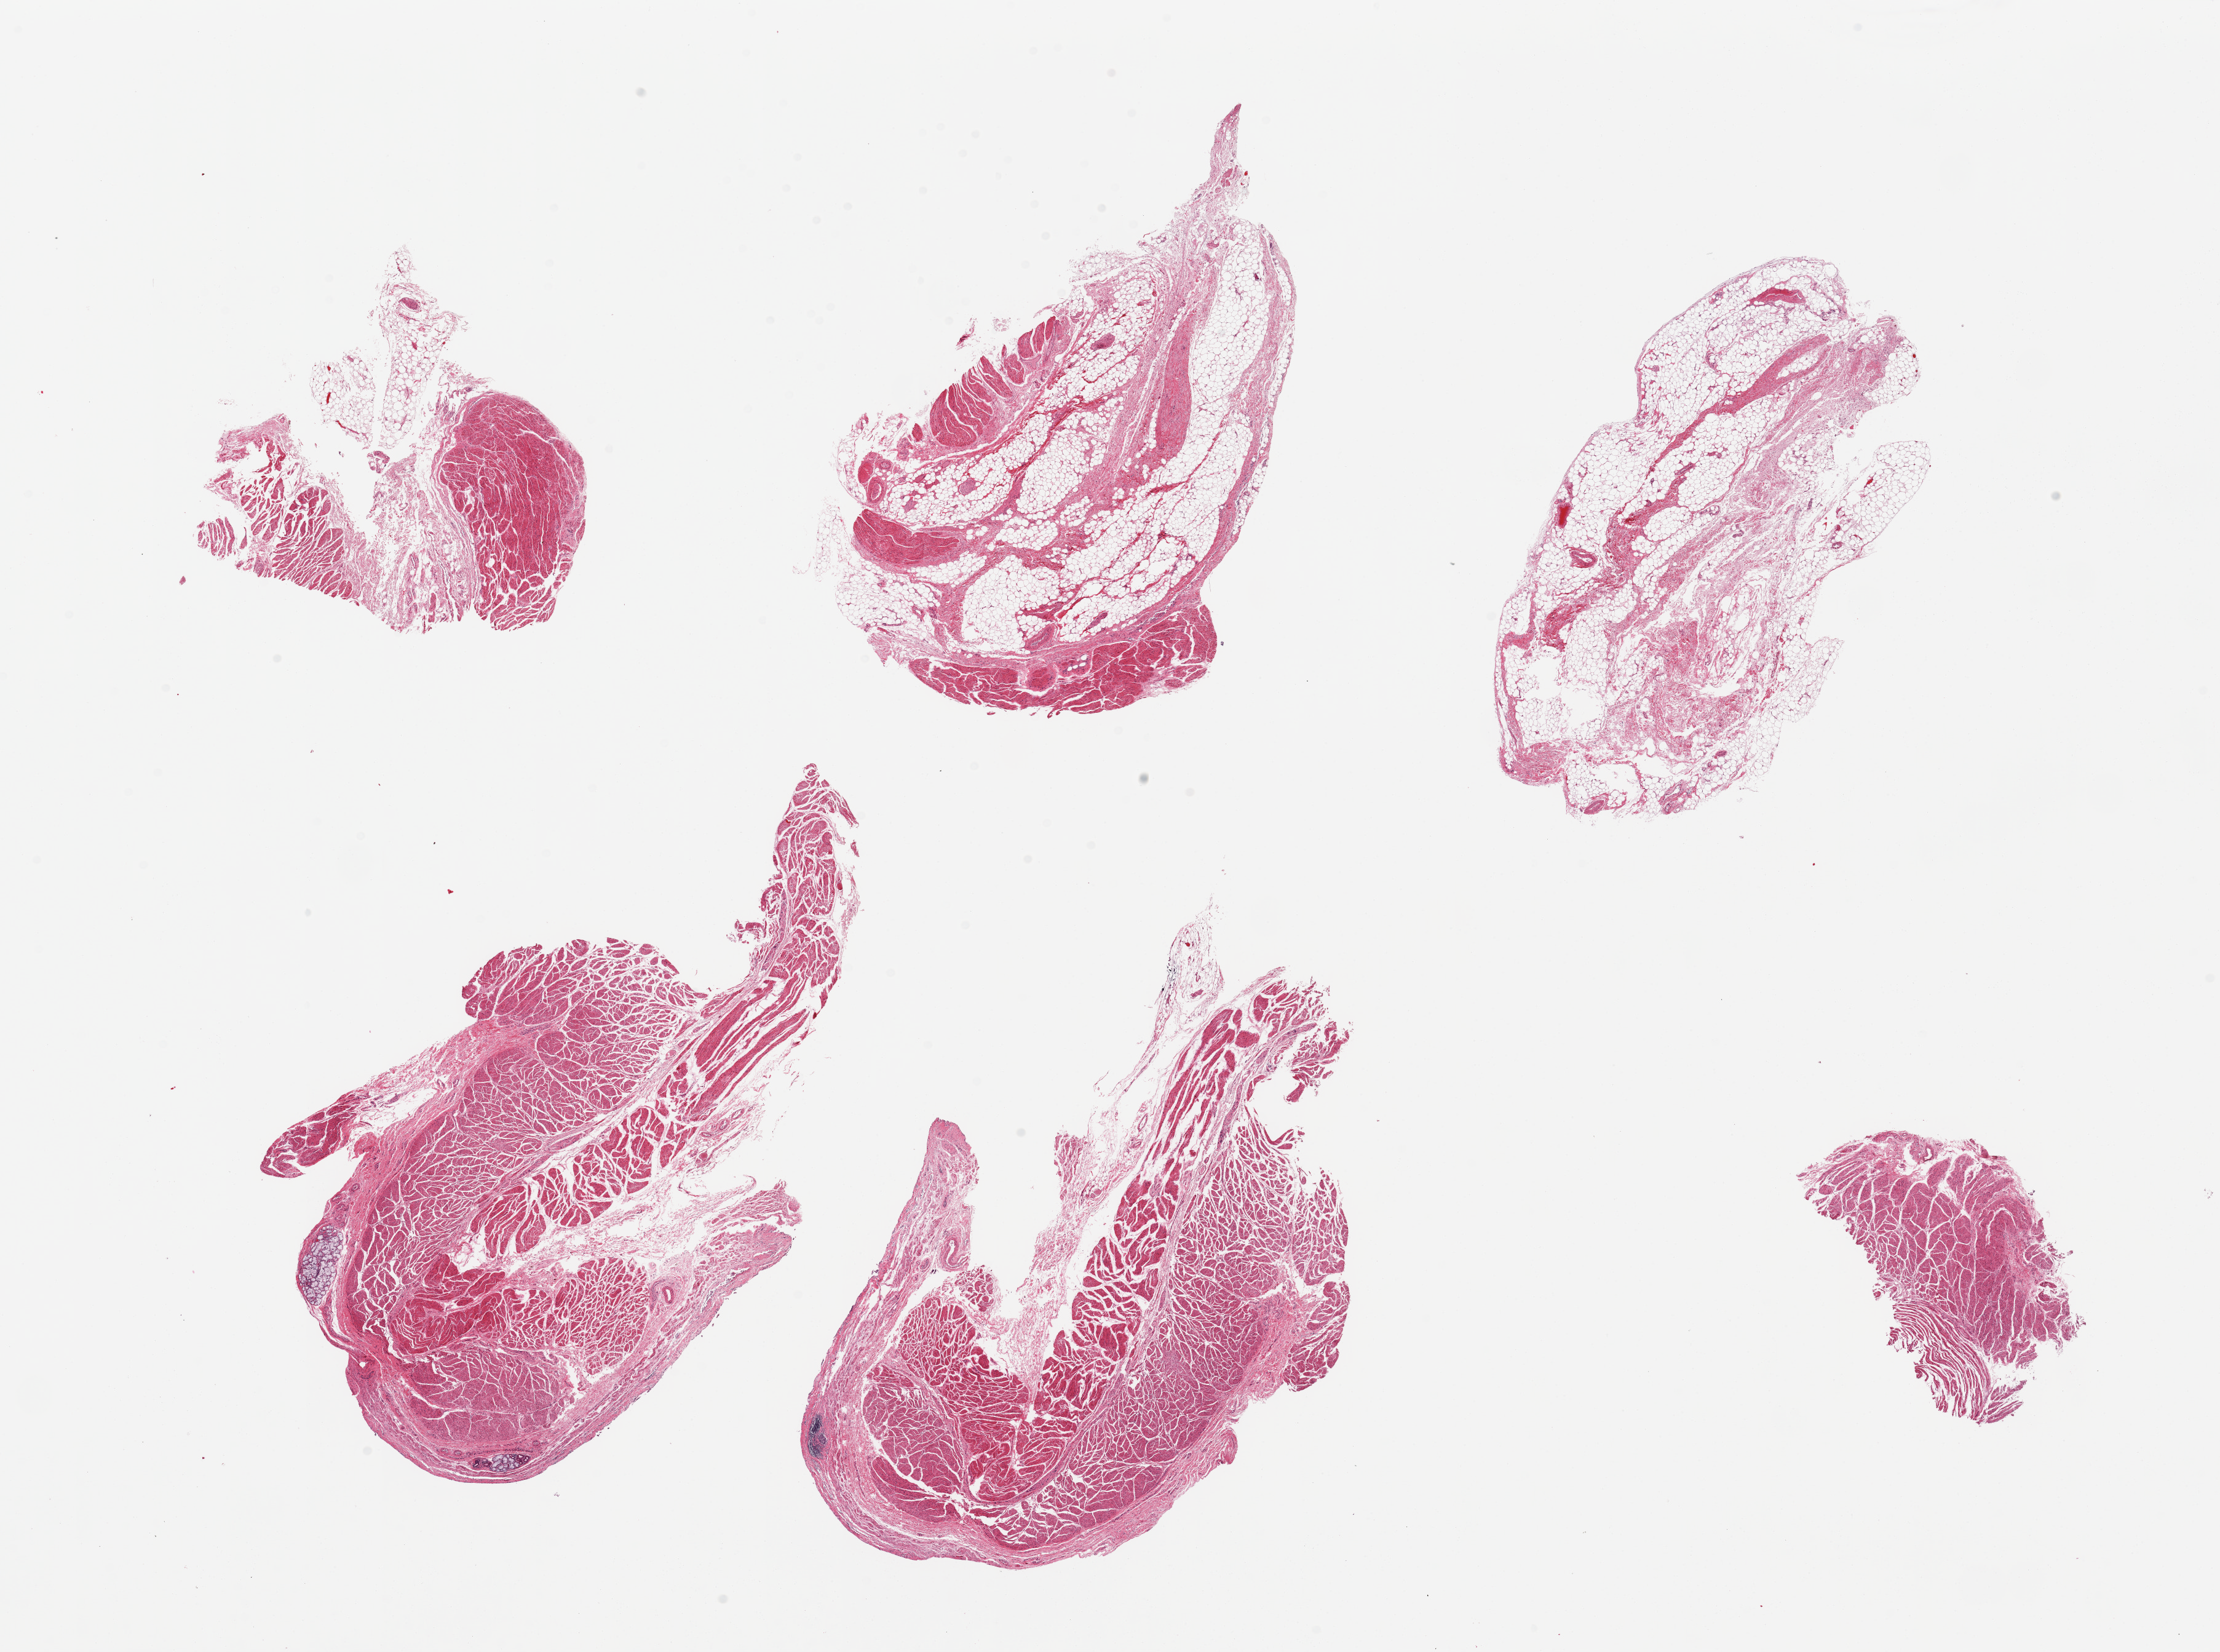
Hematoxylin and eosin (H&E) whole-slide image, brightfield, shown as a low-resolution overview of the whole scanned area (about 28.5 x 21.2 mm); PAXgene-fixed, paraffin-embedded tissue; sampled site (target tissue): esophageal muscle; donor tissue sample. Donor: male.
Reviewer comment on this tissue sample: 6 pieces; 3 are predominantly muscularis with residual submucosa/submucosal glands, 3 are mostly fat/less muscularis.